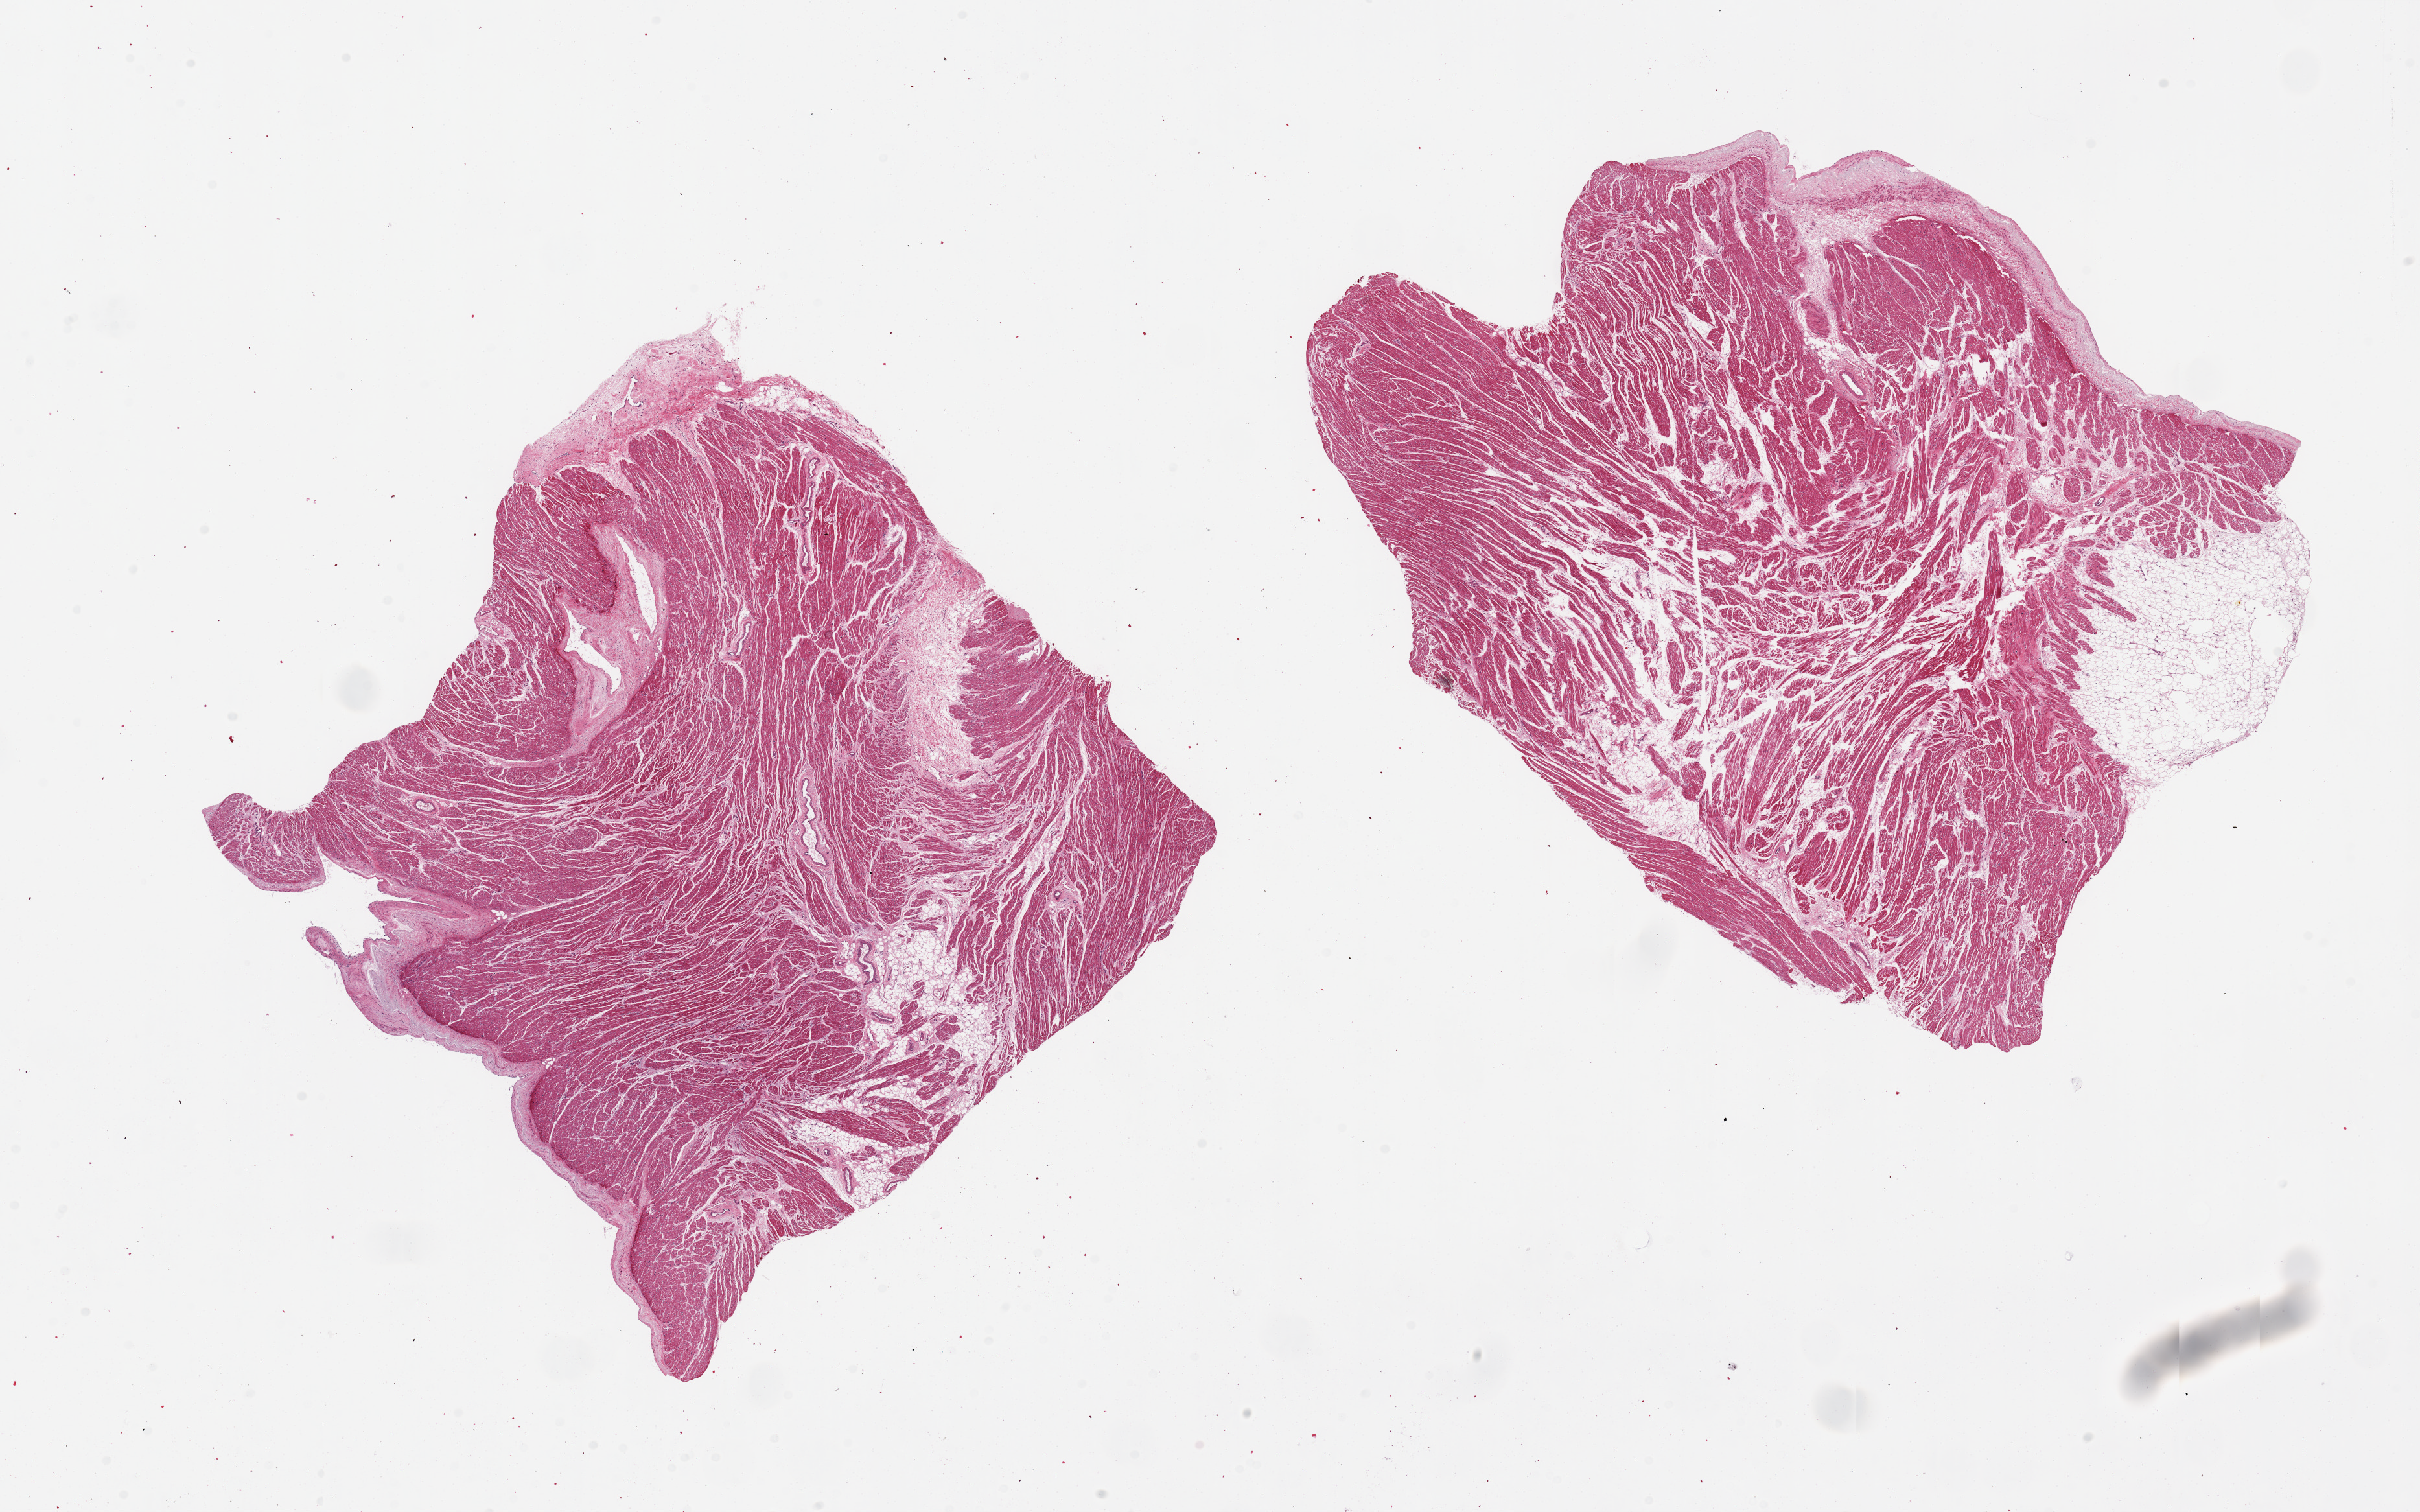
Whole-slide image, H&E stain, brightfield — whole scanned area (about 29.5 x 18.5 mm) shown as a low-resolution overview; PAXgene-fixed, paraffin-embedded tissue; sampled site (target tissue): auricular appendage; tissue donor sample. Male donor.
Reviewer comment on this tissue sample: 2 pieces, 10x10 & 13x9mm.